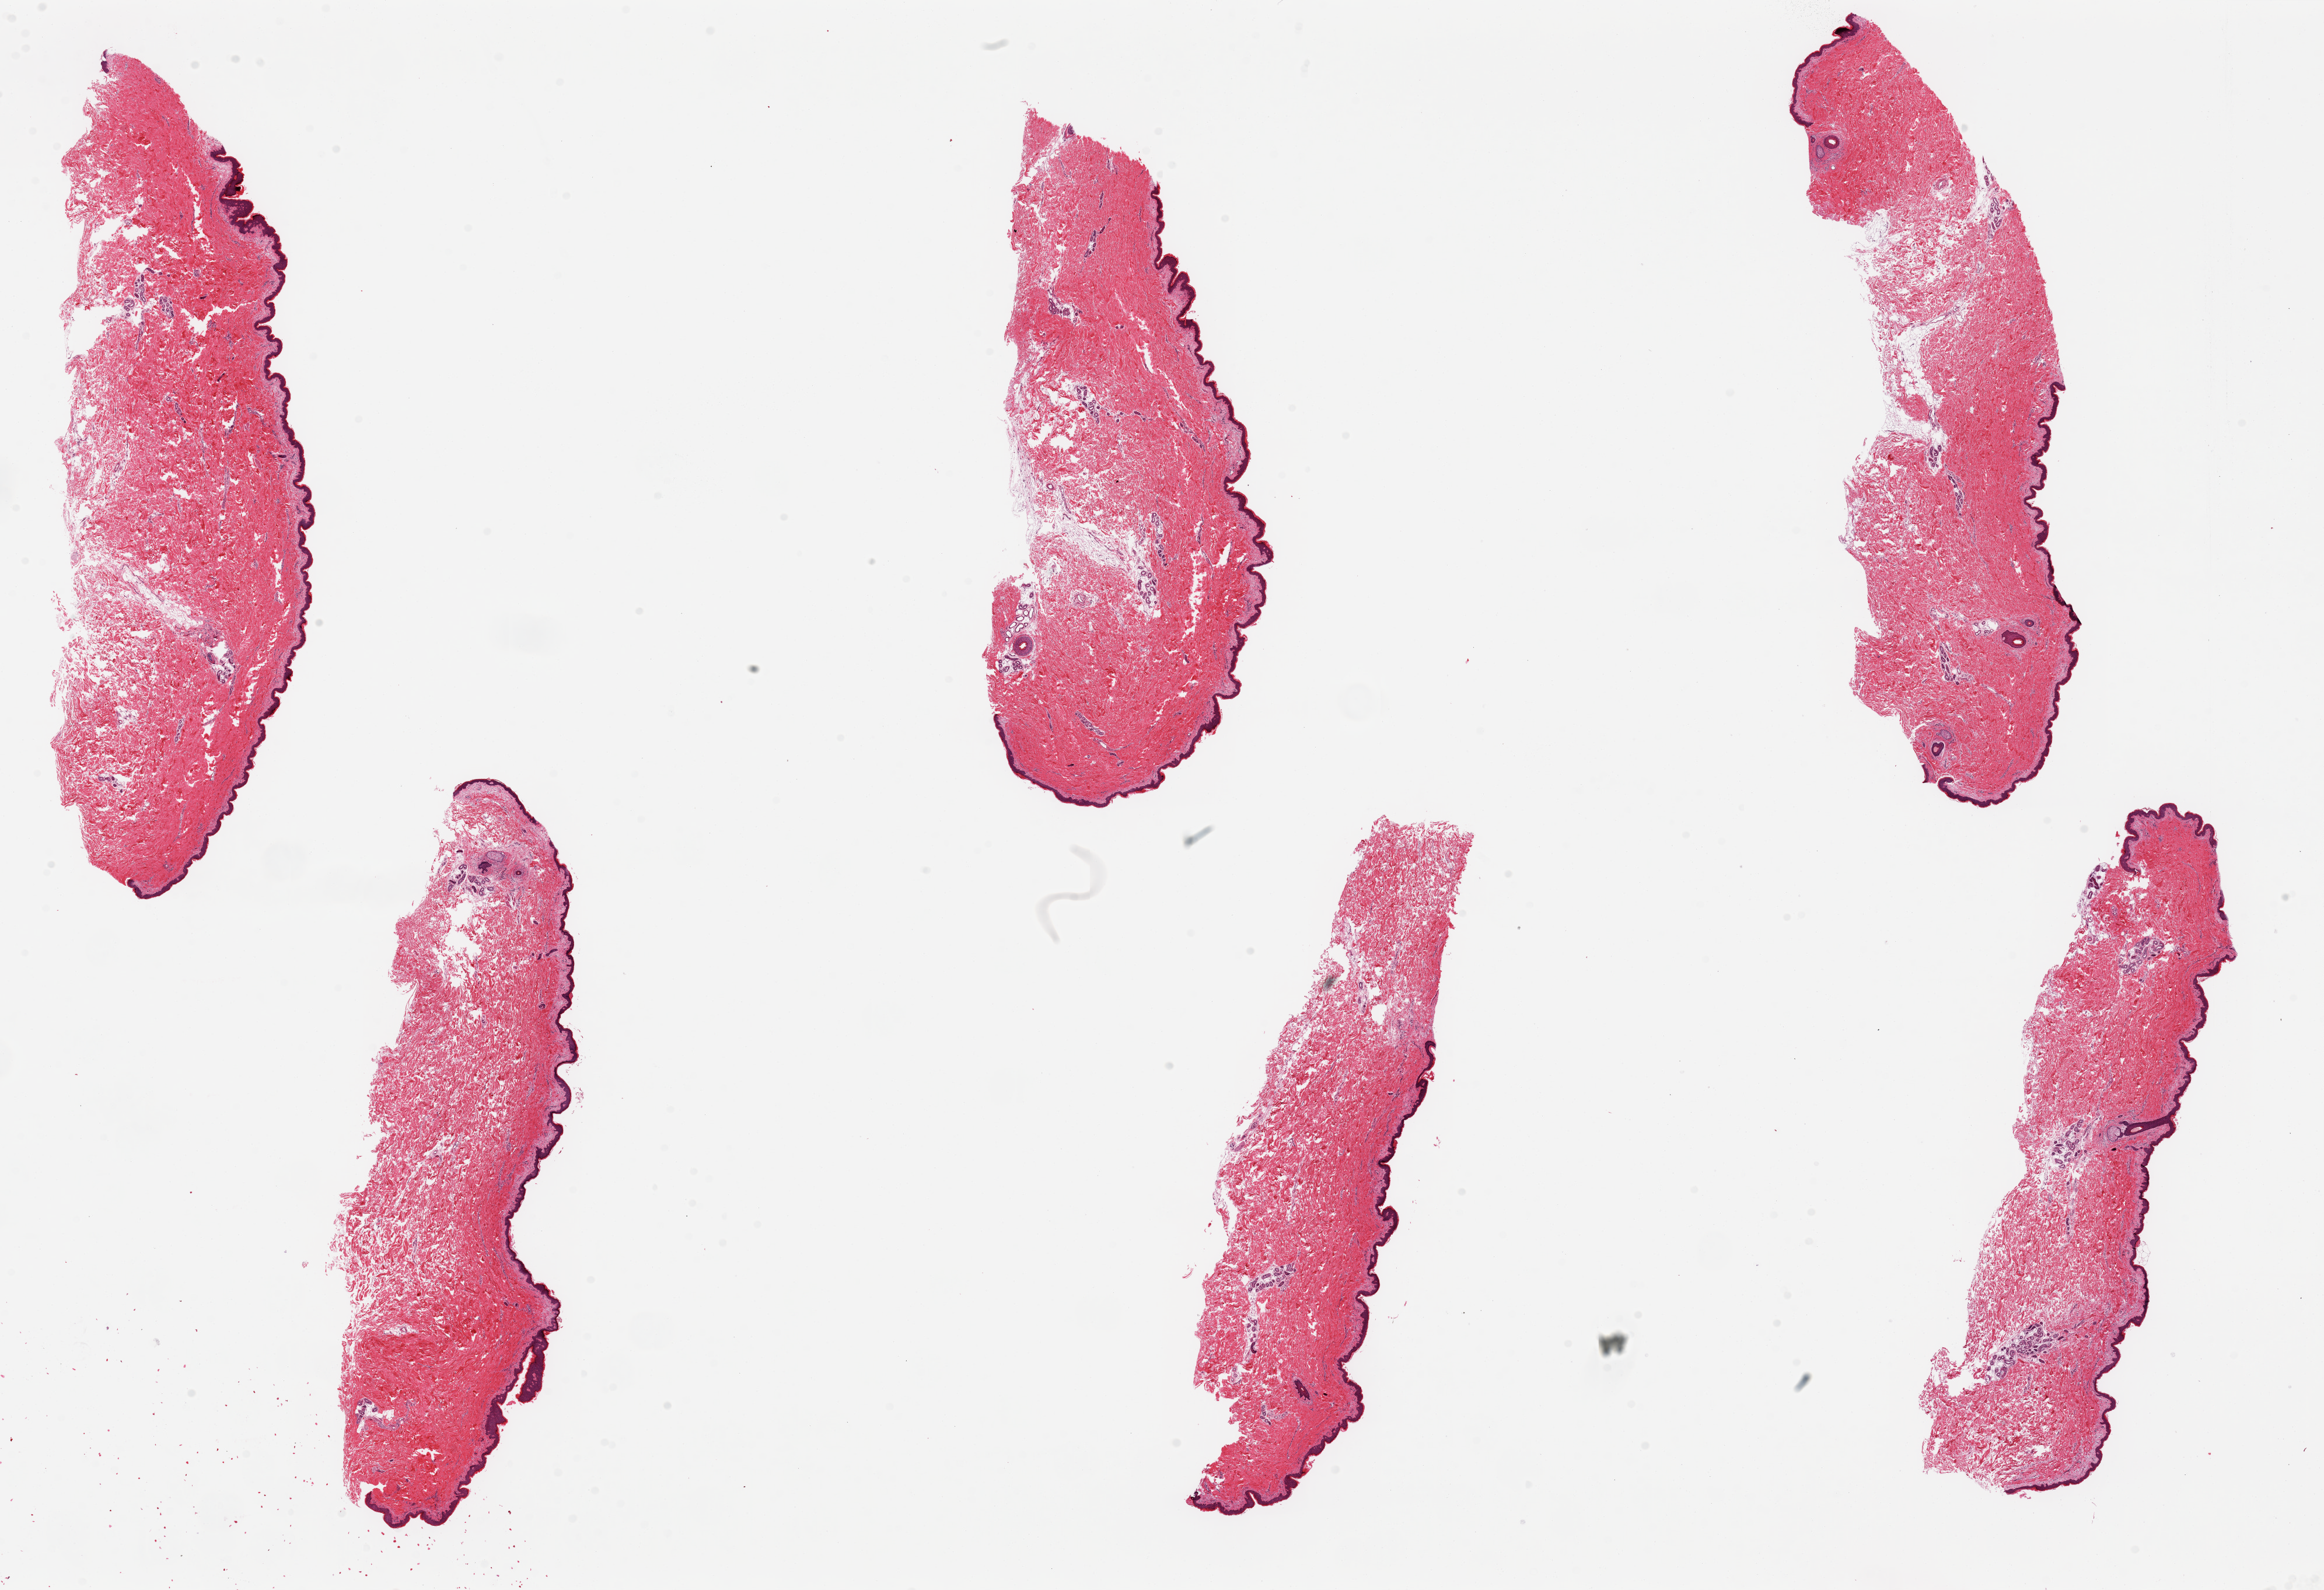
Hematoxylin and eosin (H&E) whole-slide image — low-resolution overview of the scanned area, about 31.5 x 21.6 mm. PAXgene-fixed paraffin-embedded (PFPE) section. Section of skin of suprapubic region (target tissue). Donor tissue sample.
Pathologist's review note for this sample: 6 pieces, up to 11x3.5mm; Well trimmed of subcutaneous adipose.